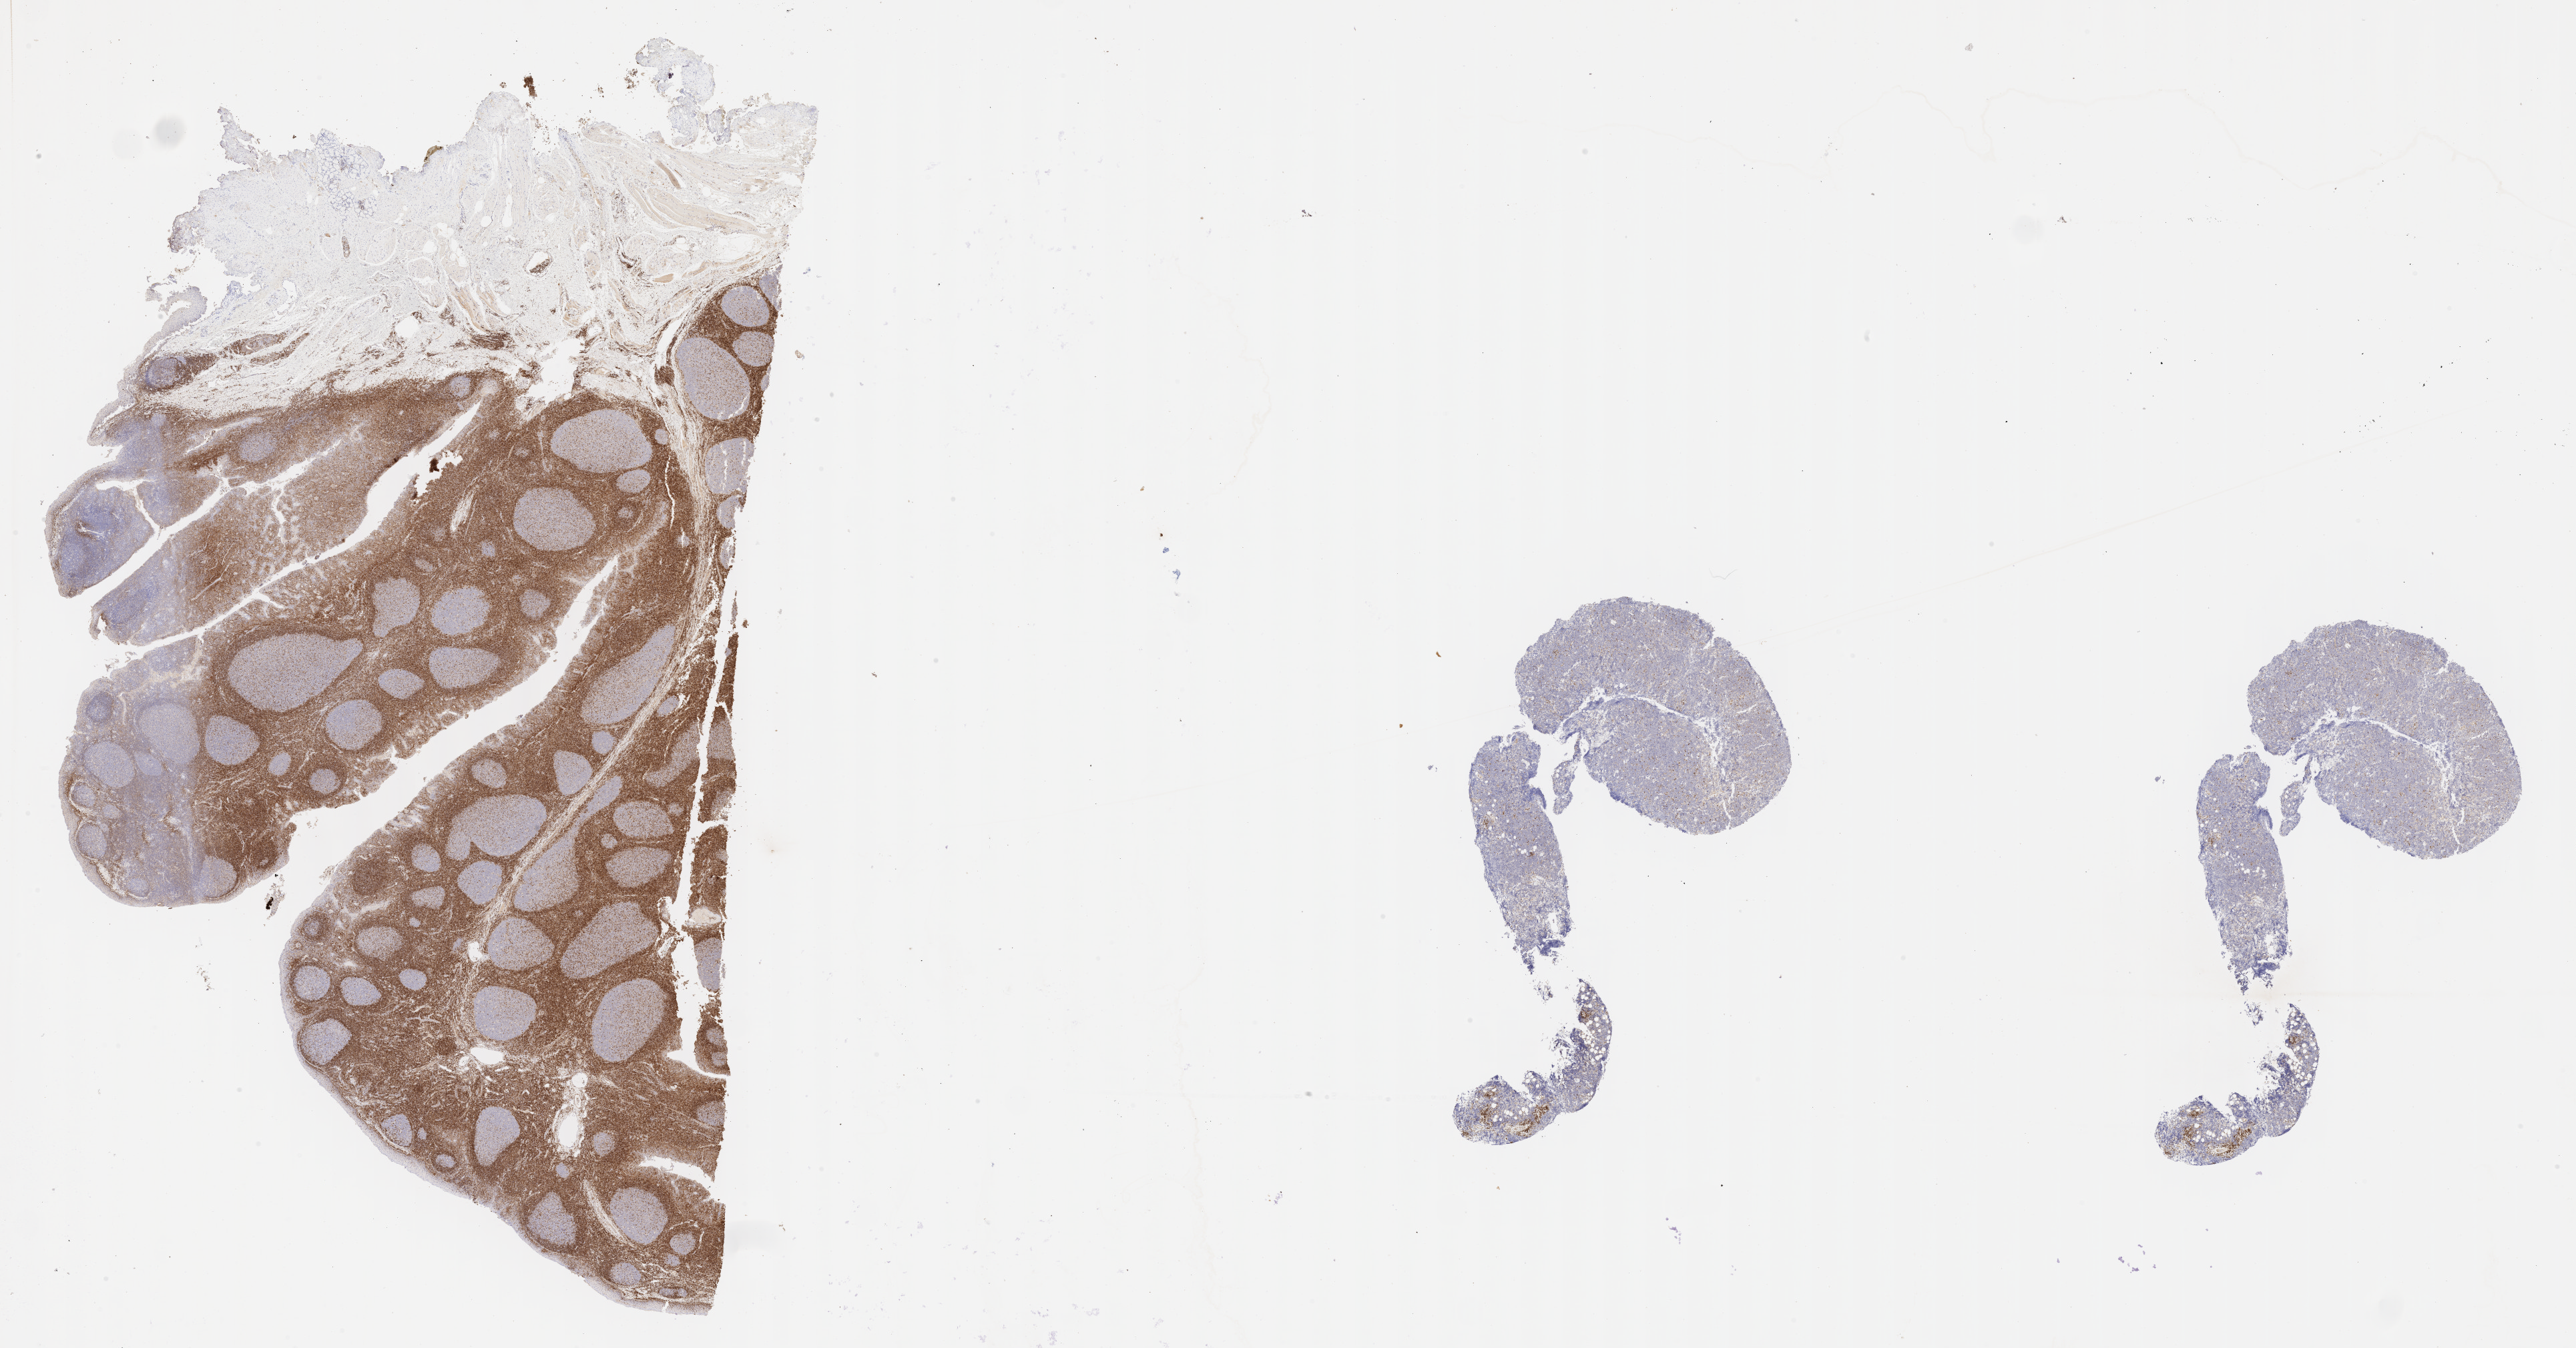
Whole-slide image, immunohistochemical stain for BCL2 — a low-resolution overview of the entire scanned area, about 31.2 x 16.3 mm. Specimen: tumor tissue. Site: head and neck. Patient: female, aged 55.
Histologic diagnosis: Burkitt lymphoma, NOS.